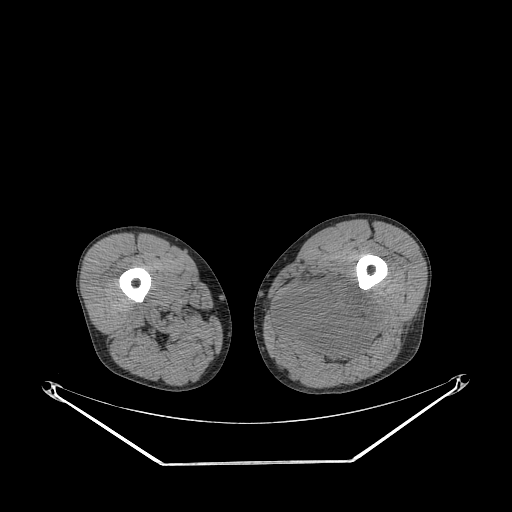
CT of an extremity soft-tissue mass (from a PET/CT study), one axial slice. Slice 237 of 267 in the series (ordered by position). Reconstruction kernel STANDARD. 140 kVp. Soft-tissue window (W 400 / L 40 HU). 3.75 mm slice thickness. 512 × 512 image matrix. Male patient. From the clinical record (not read from this slice): histological type: undifferentiated pleomorphic liposarcoma; grade: high; site of the primary tumour: left thigh.
Outlined on this slice (expert contour drawn on MRI and transferred to this co-registered scan by the dataset authors):
- gross tumour volume including surrounding oedema: bounding box <276,281,378,362> (left, top, right, bottom; pixels)
- gross tumour volume (mass): <276,281,378,359>